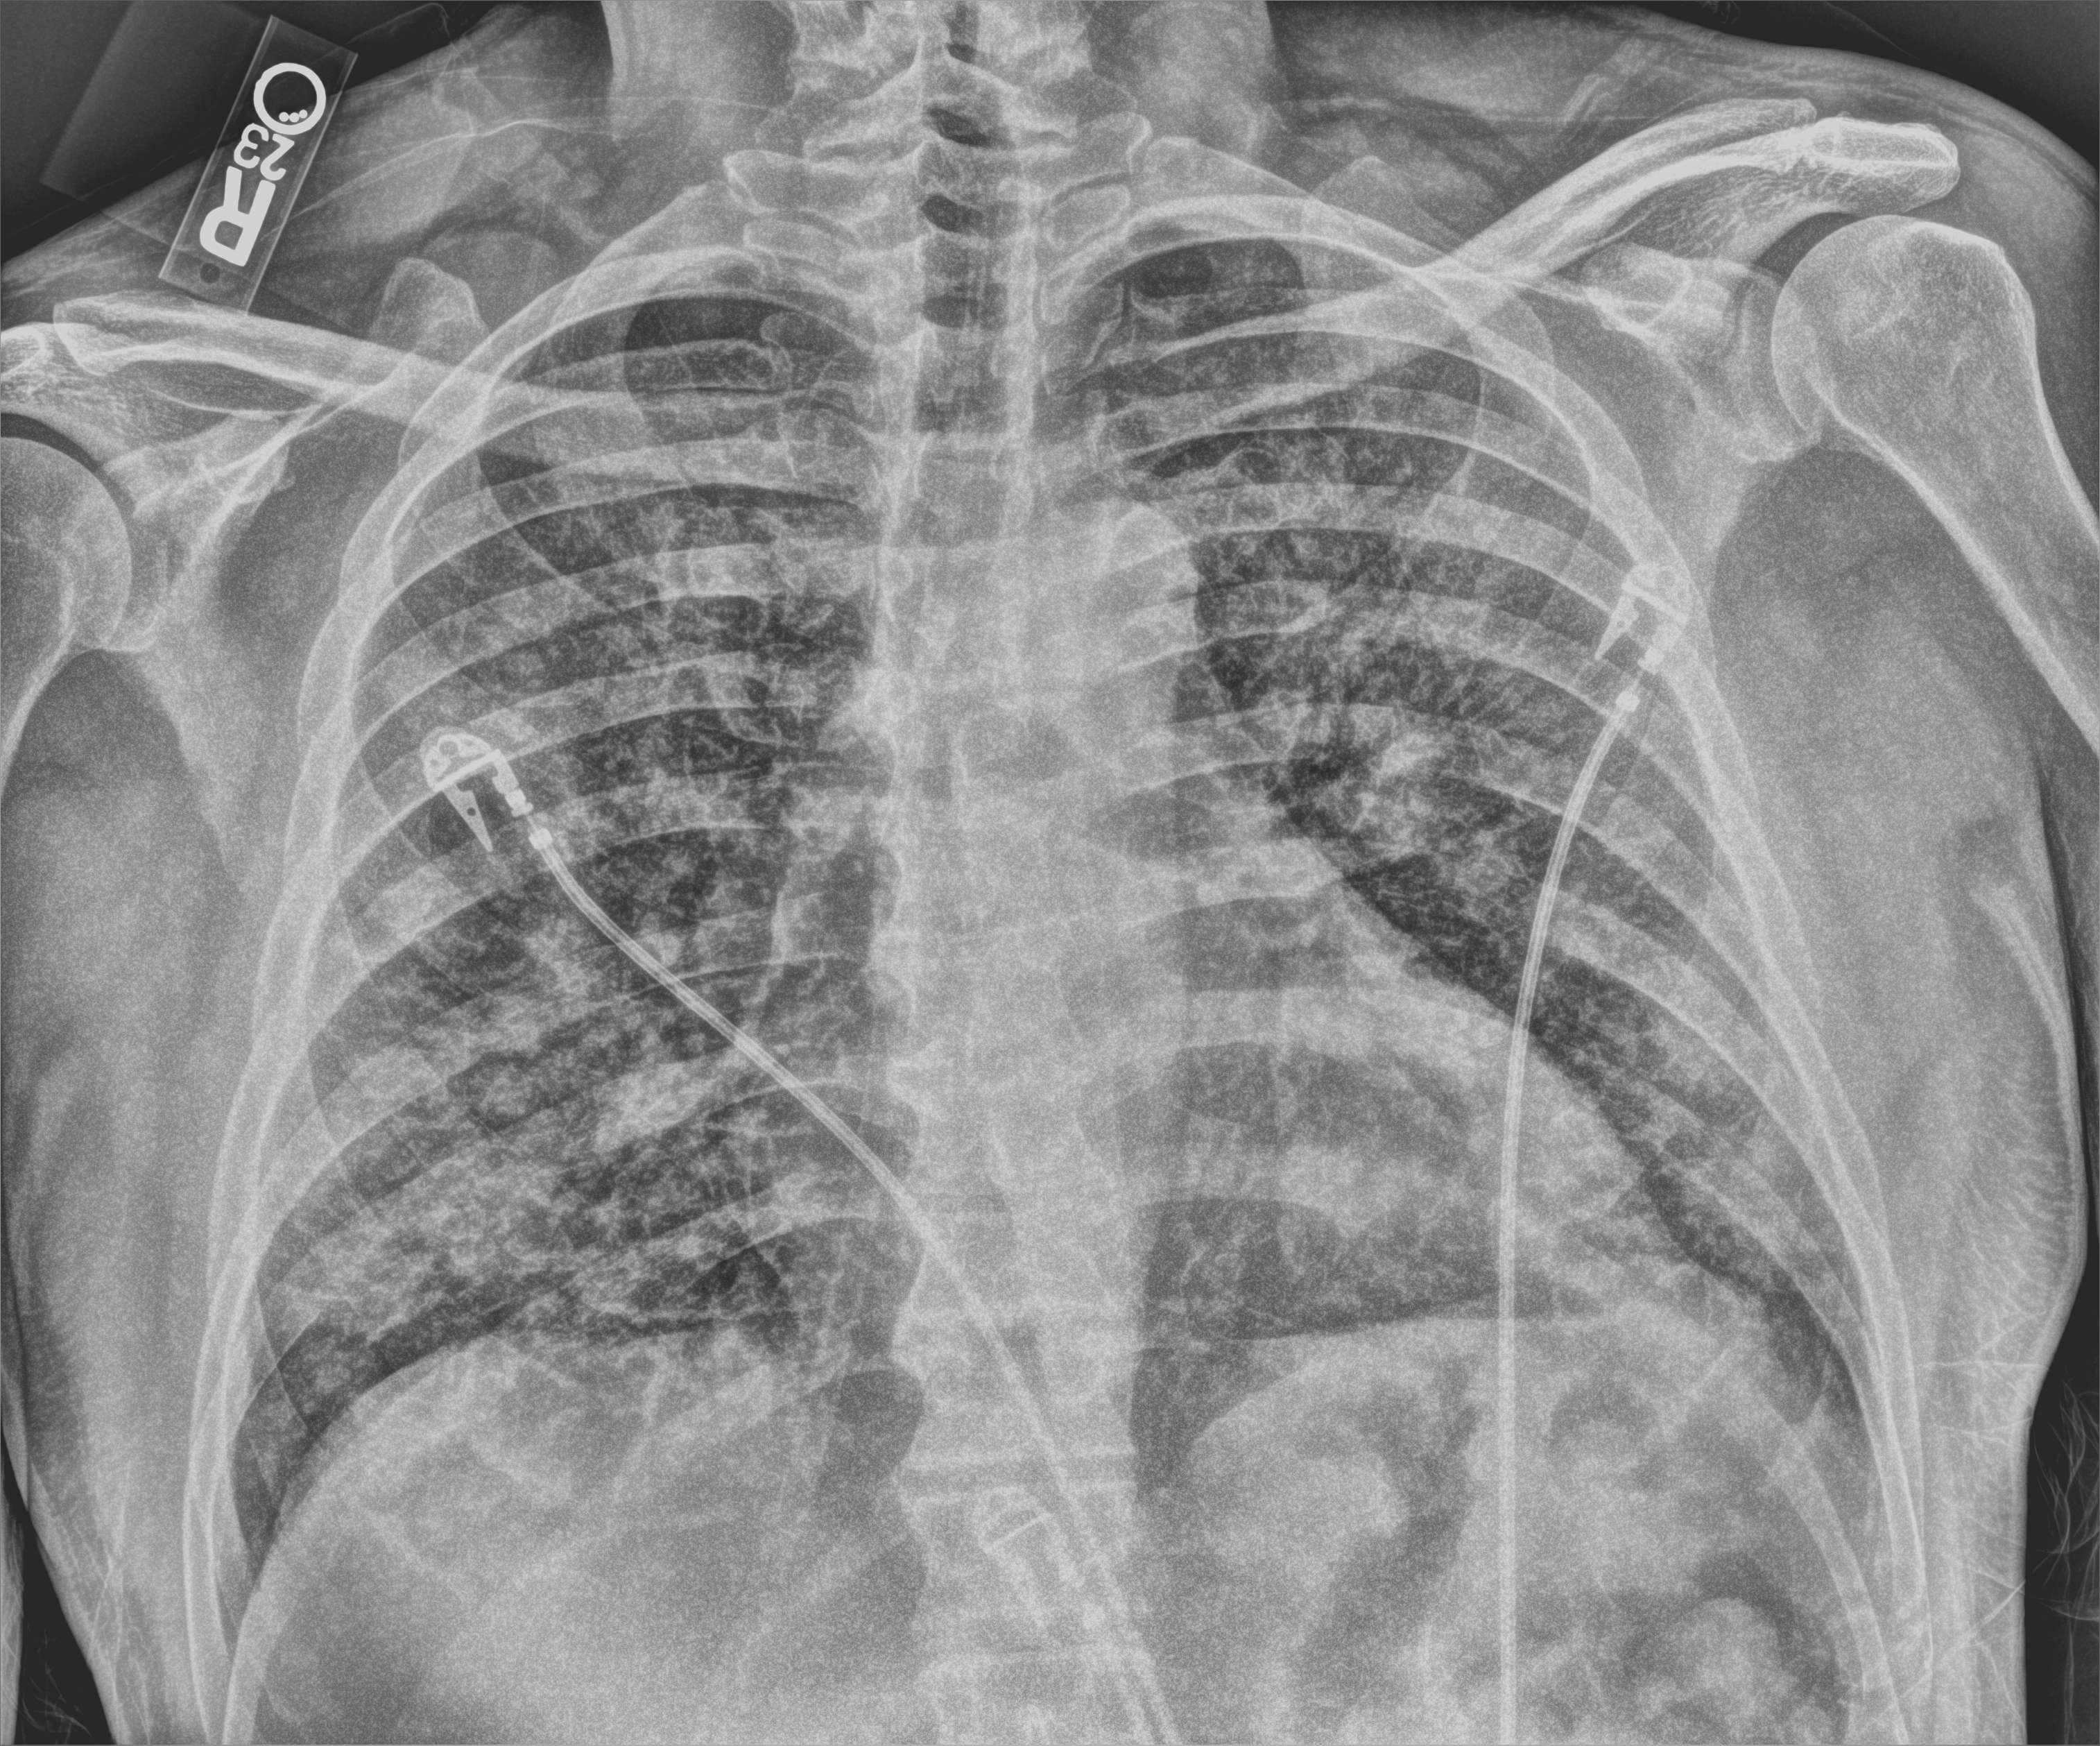
Bedside chest radiograph (computed radiography), anteroposterior (AP) projection. Patient hospitalised with COVID-19; male, aged 18–59 years.
Admission-level facts for this patient (not findings on this image; timing relative to this image not recorded): admitted to intensive care during this hospital stay: no; mechanically ventilated during this hospital stay: no; length of hospital stay: 7 days.